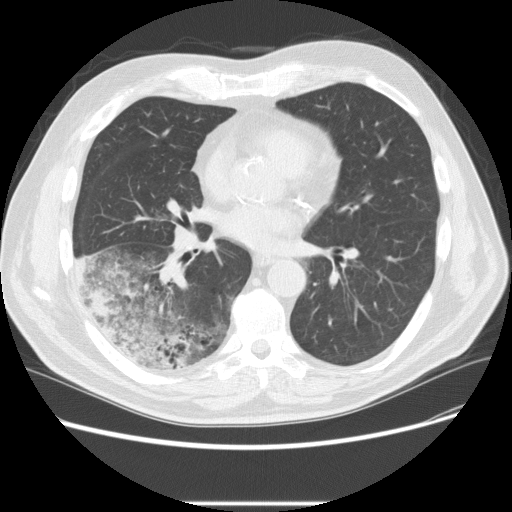
Low-dose screening chest CT, one axial slice. Position 107 of 233 along the scan axis. Reconstruction kernel STANDARD. Lung window (W 1500 / L -600 HU). 2.5 mm slice thickness. 512 × 512 image matrix.
Structures marked on this image (expert manual segmentation):
- lesion 3 (tumor, lower lobe of right lung): bounding box (x1, y1, x2, y2) in pixels: (92, 282, 124, 317)